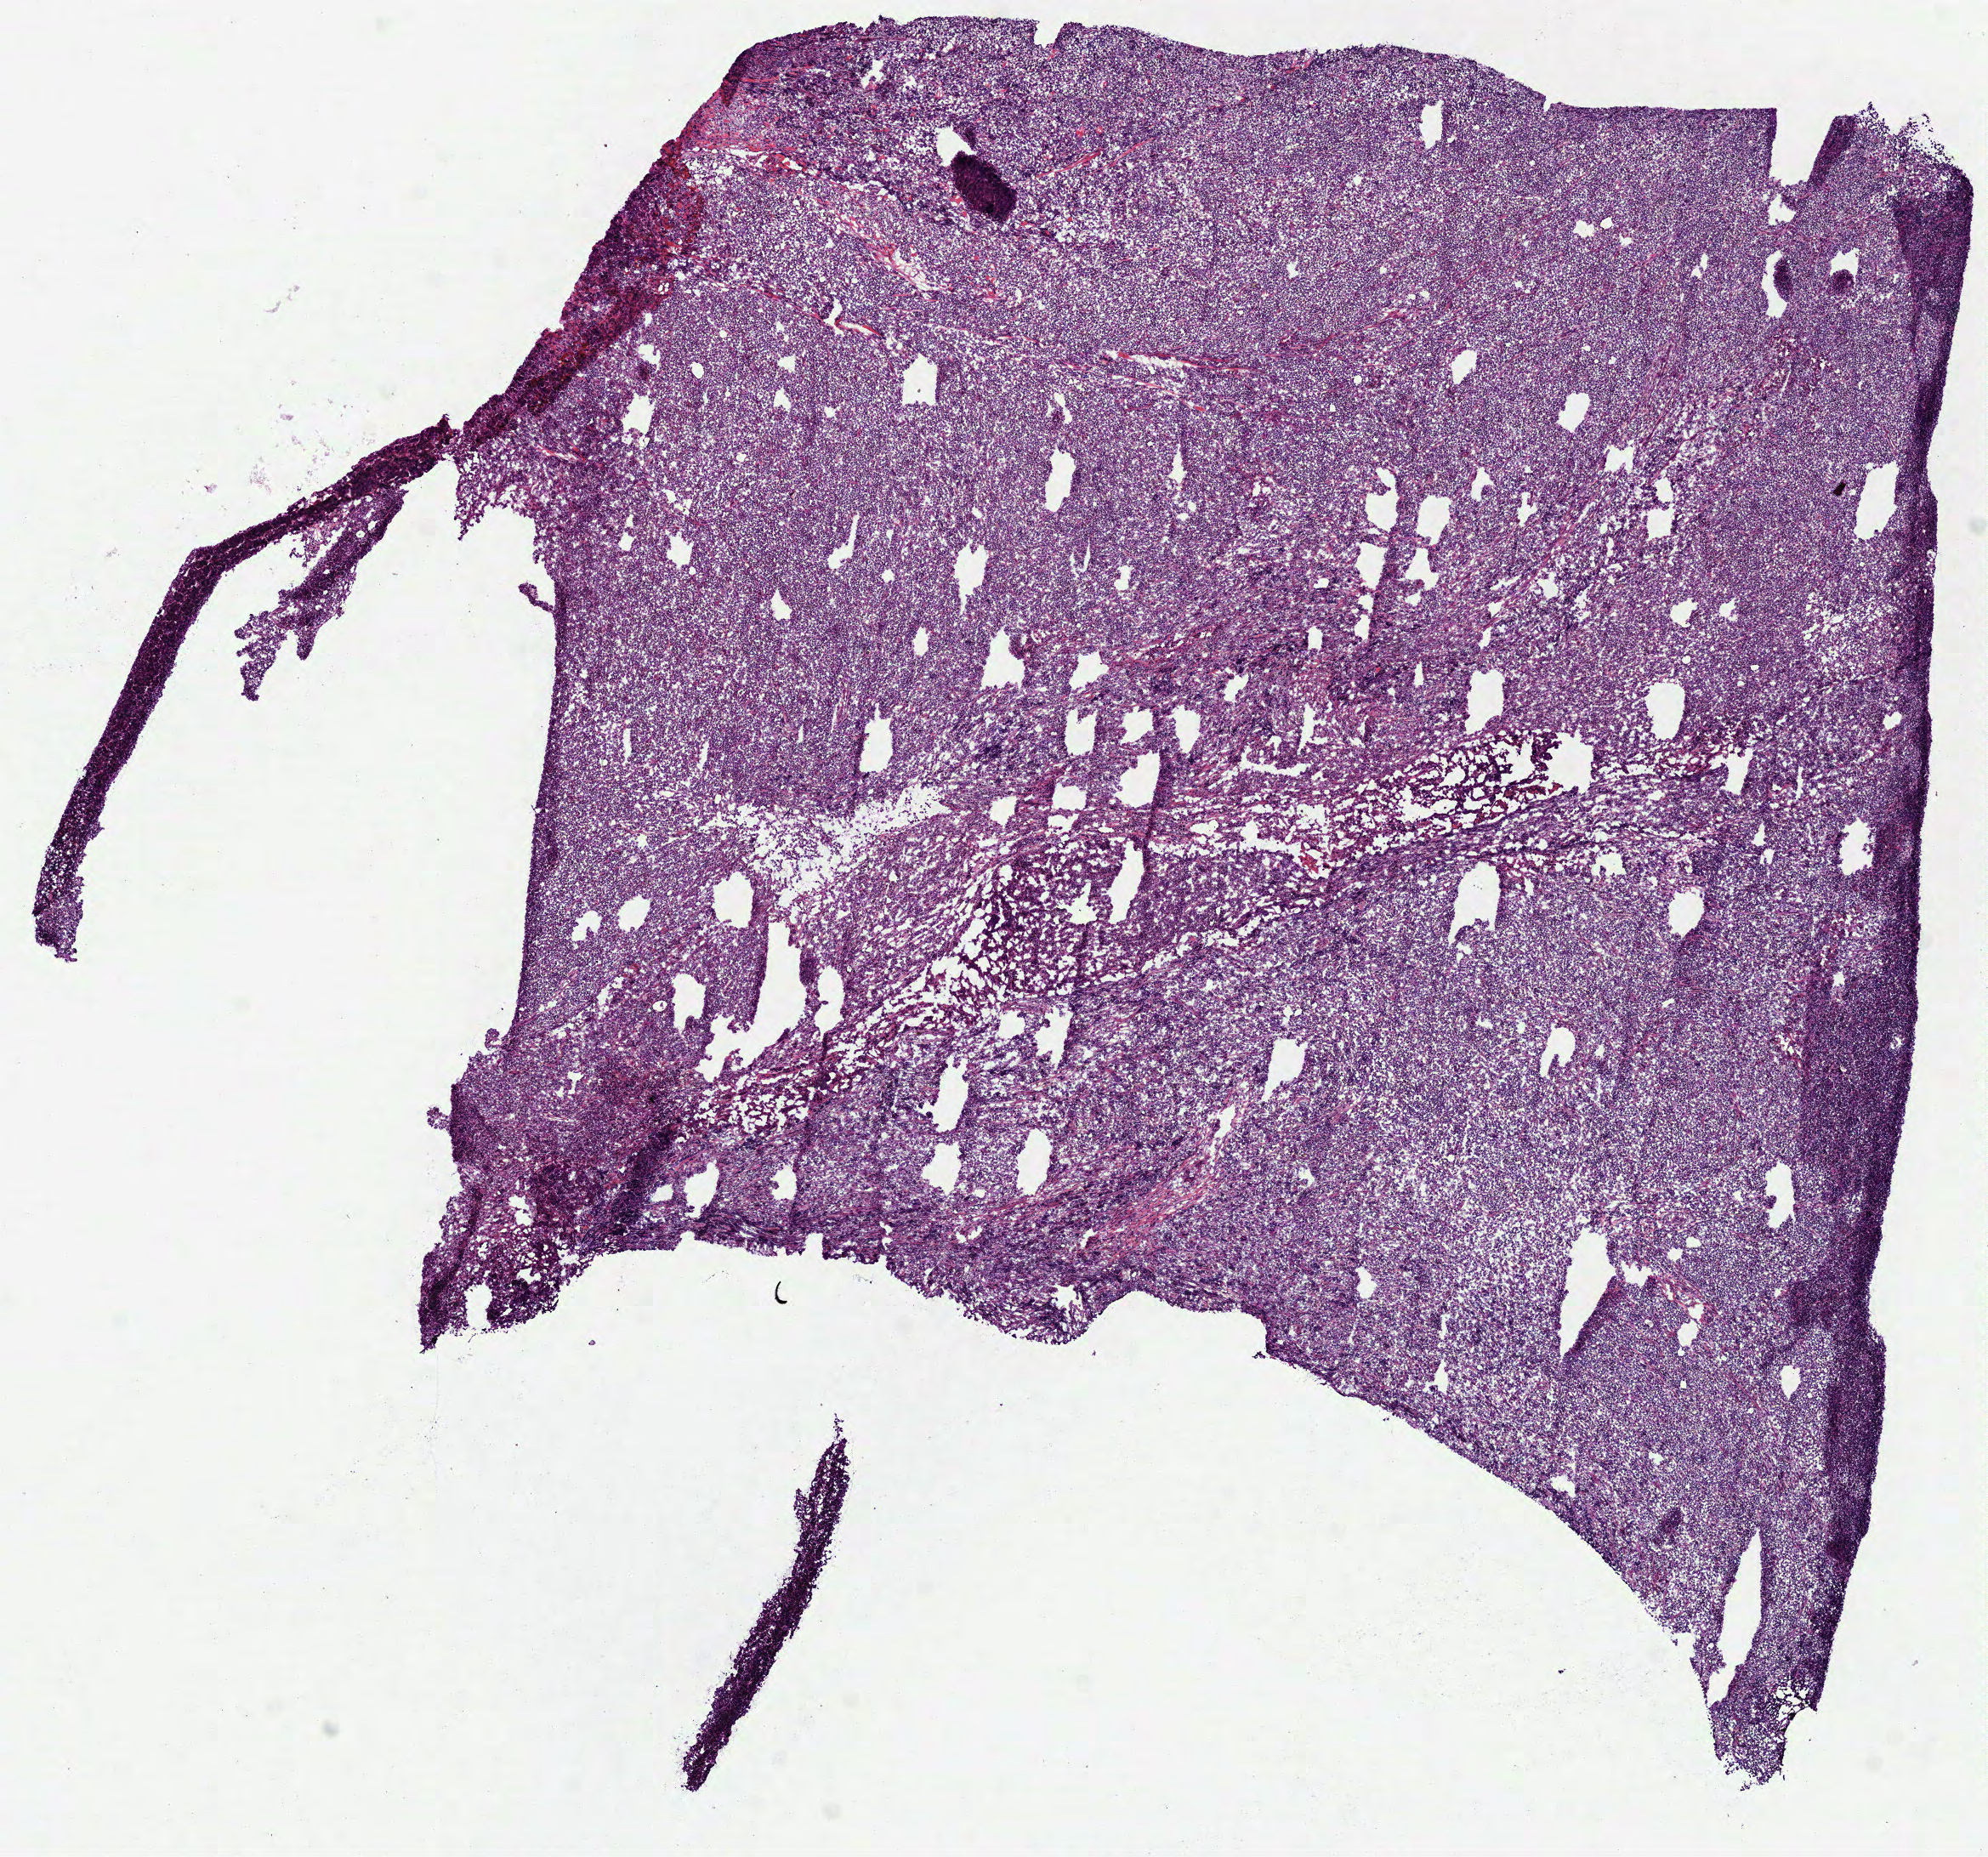
H&E-stained whole-slide image — low-resolution overview of the scanned area, about 9.4 x 8.8 mm (acquisition: 40x scan). Frozen section from the bottom of the tissue portion. Primary tumour sample from the lymphoid tissue. Patient: female, age at initial diagnosis 57 years. Pathologist review of this section (percent, as recorded): tumour cells 100%, tumour nuclei 90%, normal cells 0%, stromal cells 0%, necrosis 0%. Inflammatory infiltration, as recorded: lymphocyte infiltration 9%.
Diagnosis: Diffuse large B-cell lymphoma, NOS.